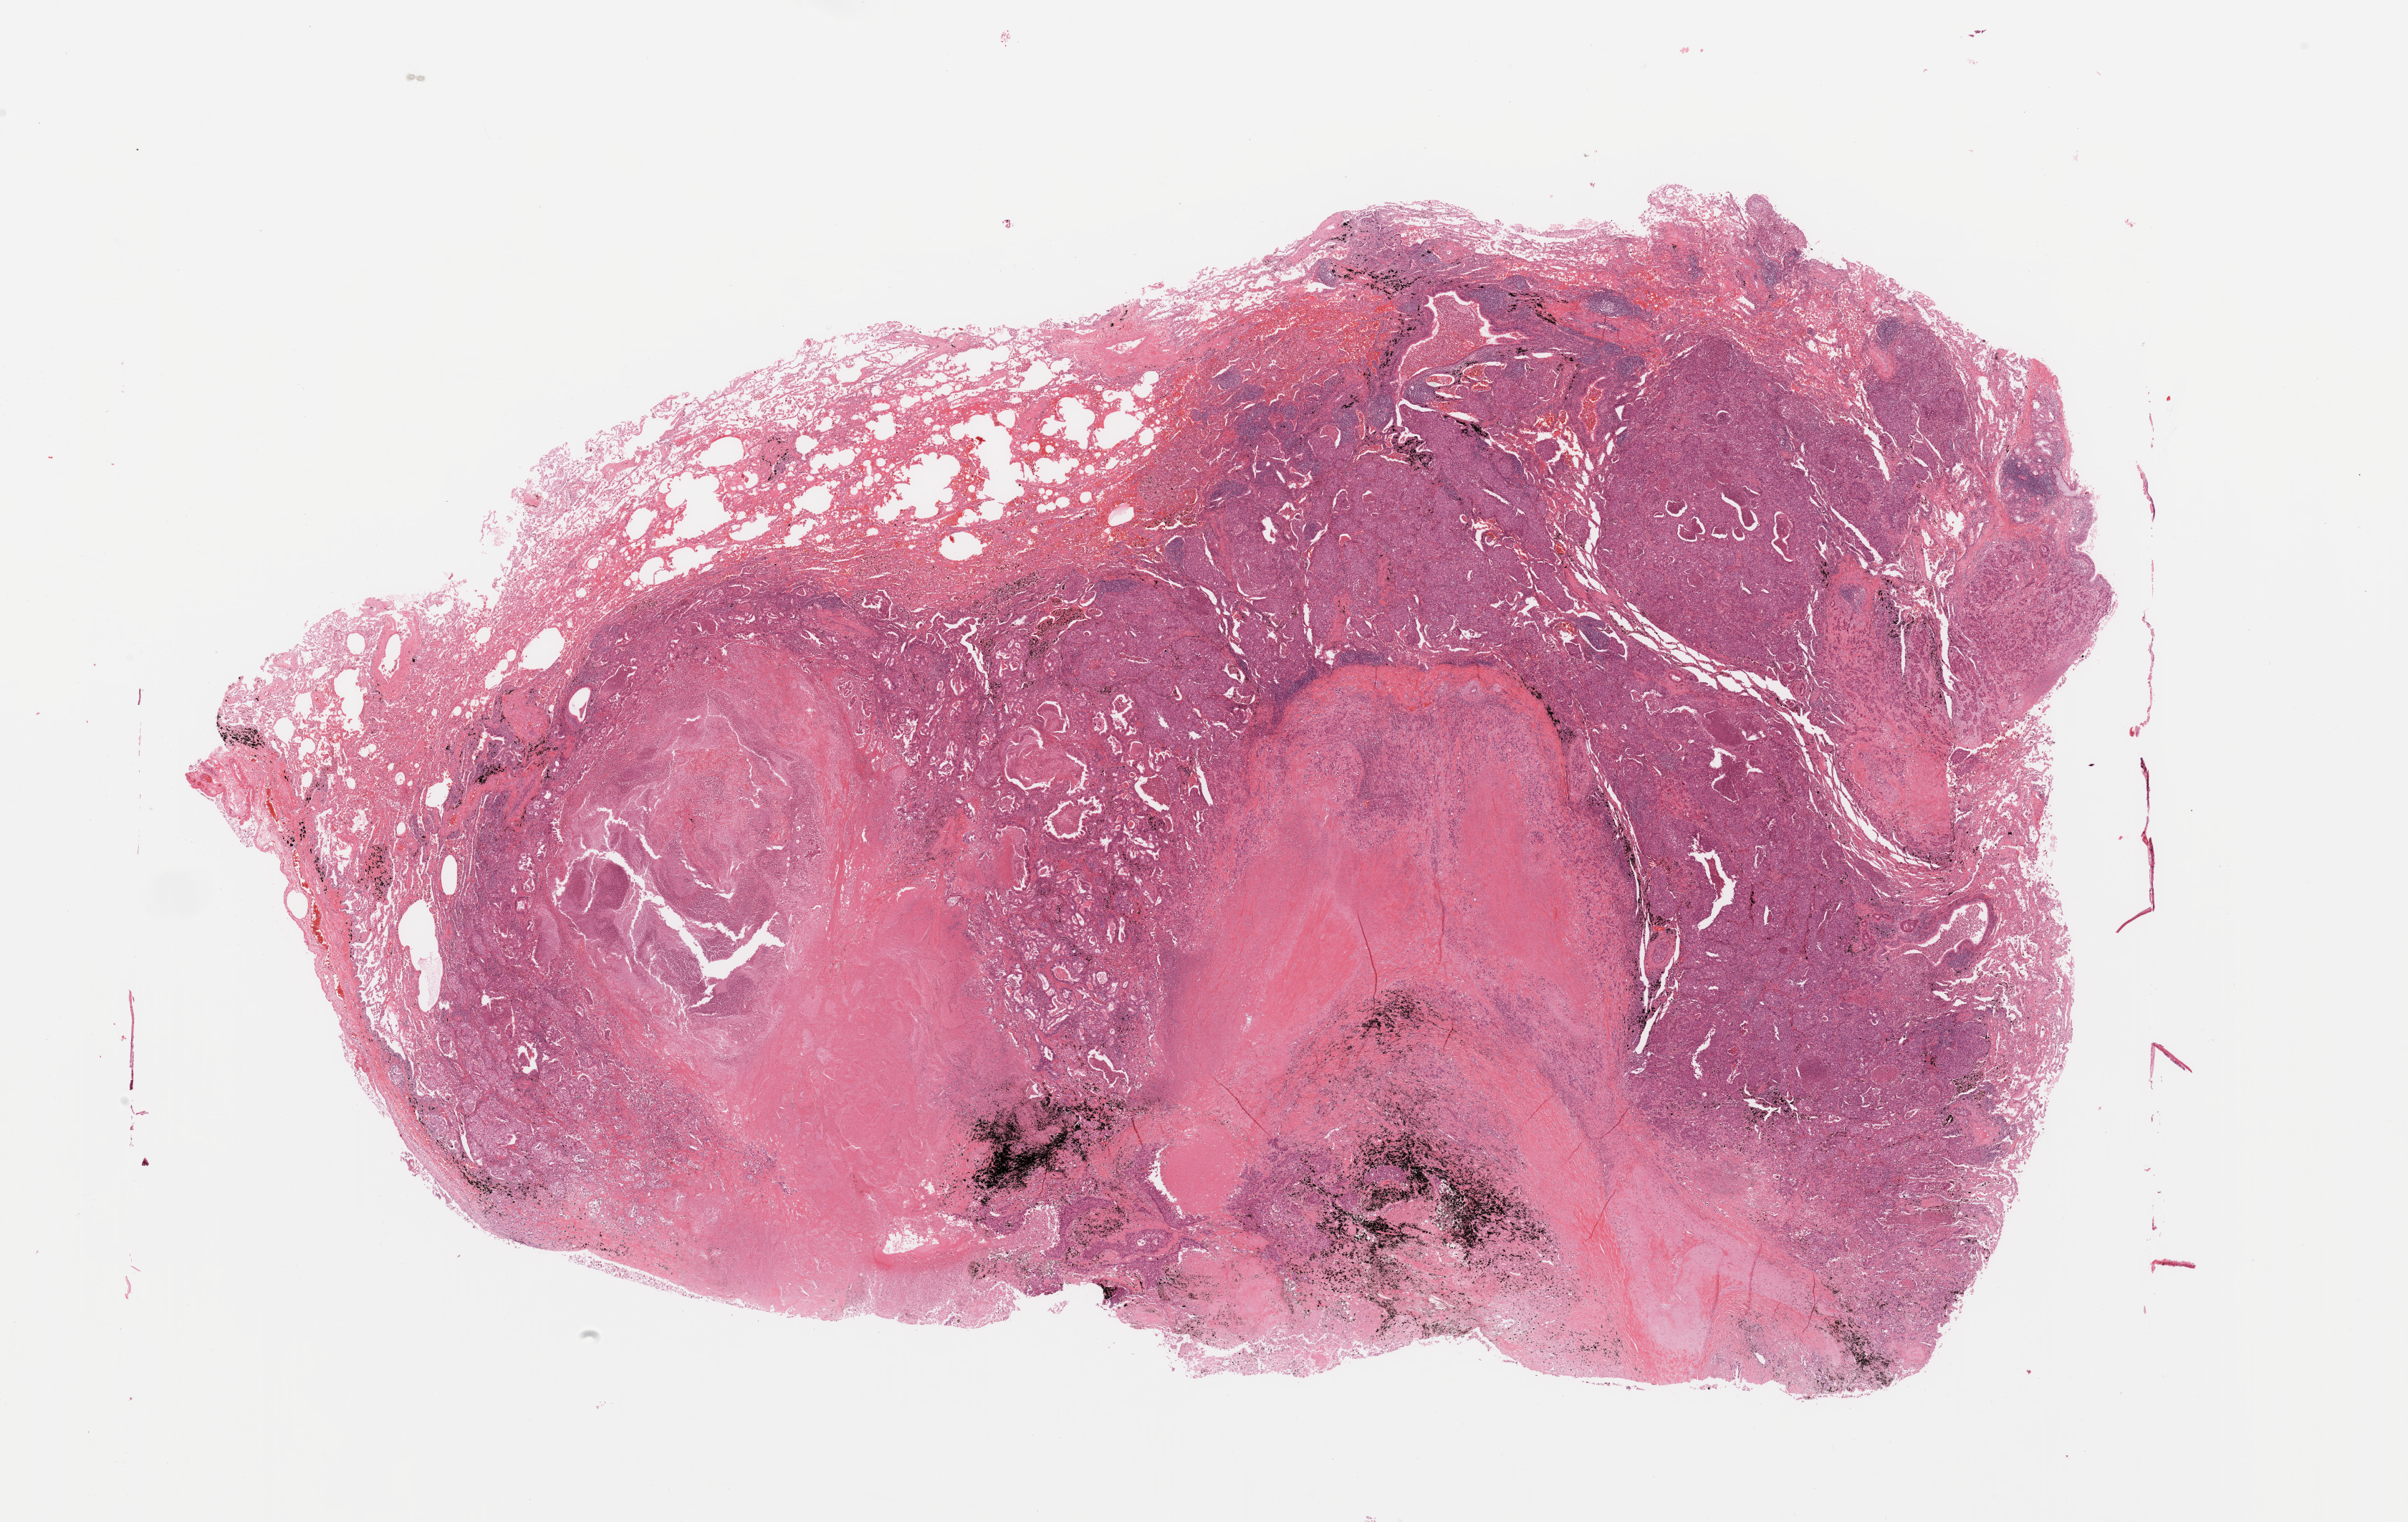
Hematoxylin and eosin (H&E) stained whole-slide image — whole scanned area (about 26.6 x 16.8 mm, acquisition: 20x scan) shown as a low-resolution overview. Lung, tumour tissue. Male, 64 y/o.
Patient diagnosis (cohort enrolment): squamous cell carcinoma (lung).